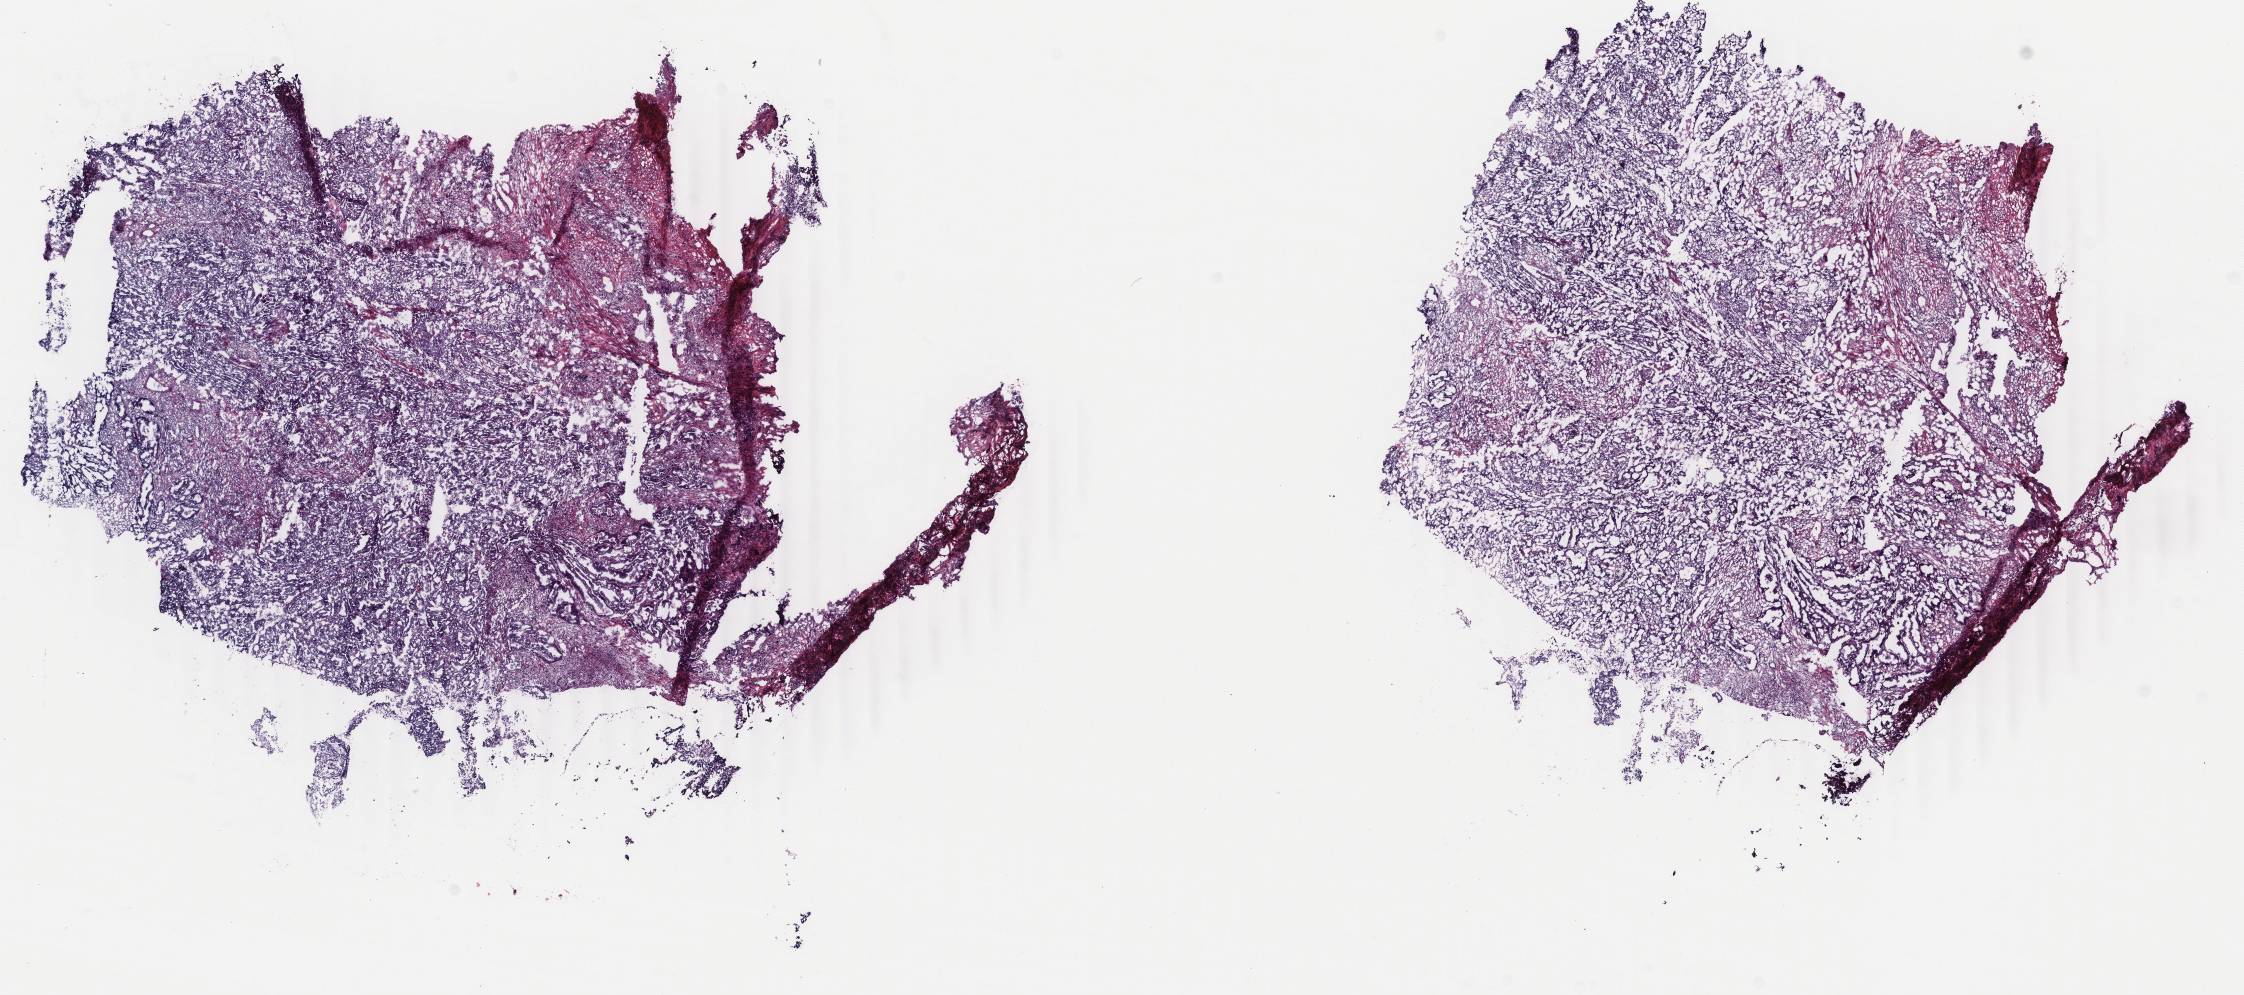
H&E-stained whole-slide image, low-resolution overview of the scanned area, about 17.8 x 7.9 mm (slide scanned at 40x), frozen section, uterus, primary tumour sample. Patient: female, age at initial diagnosis 60 years. Histologic grade: G2 (moderately differentiated). Composition of this section per pathologist review: tumour cells 70%, tumour nuclei 100%, normal cells 10%, stromal cells 0%, necrosis 20%. Infiltration values recorded for this section: lymphocyte infiltration 10%, monocyte infiltration 0%, neutrophil infiltration 0%.
- FIGO stage: IIIA
- histologic diagnosis: Endometrioid adenocarcinoma, NOS (endometrium)